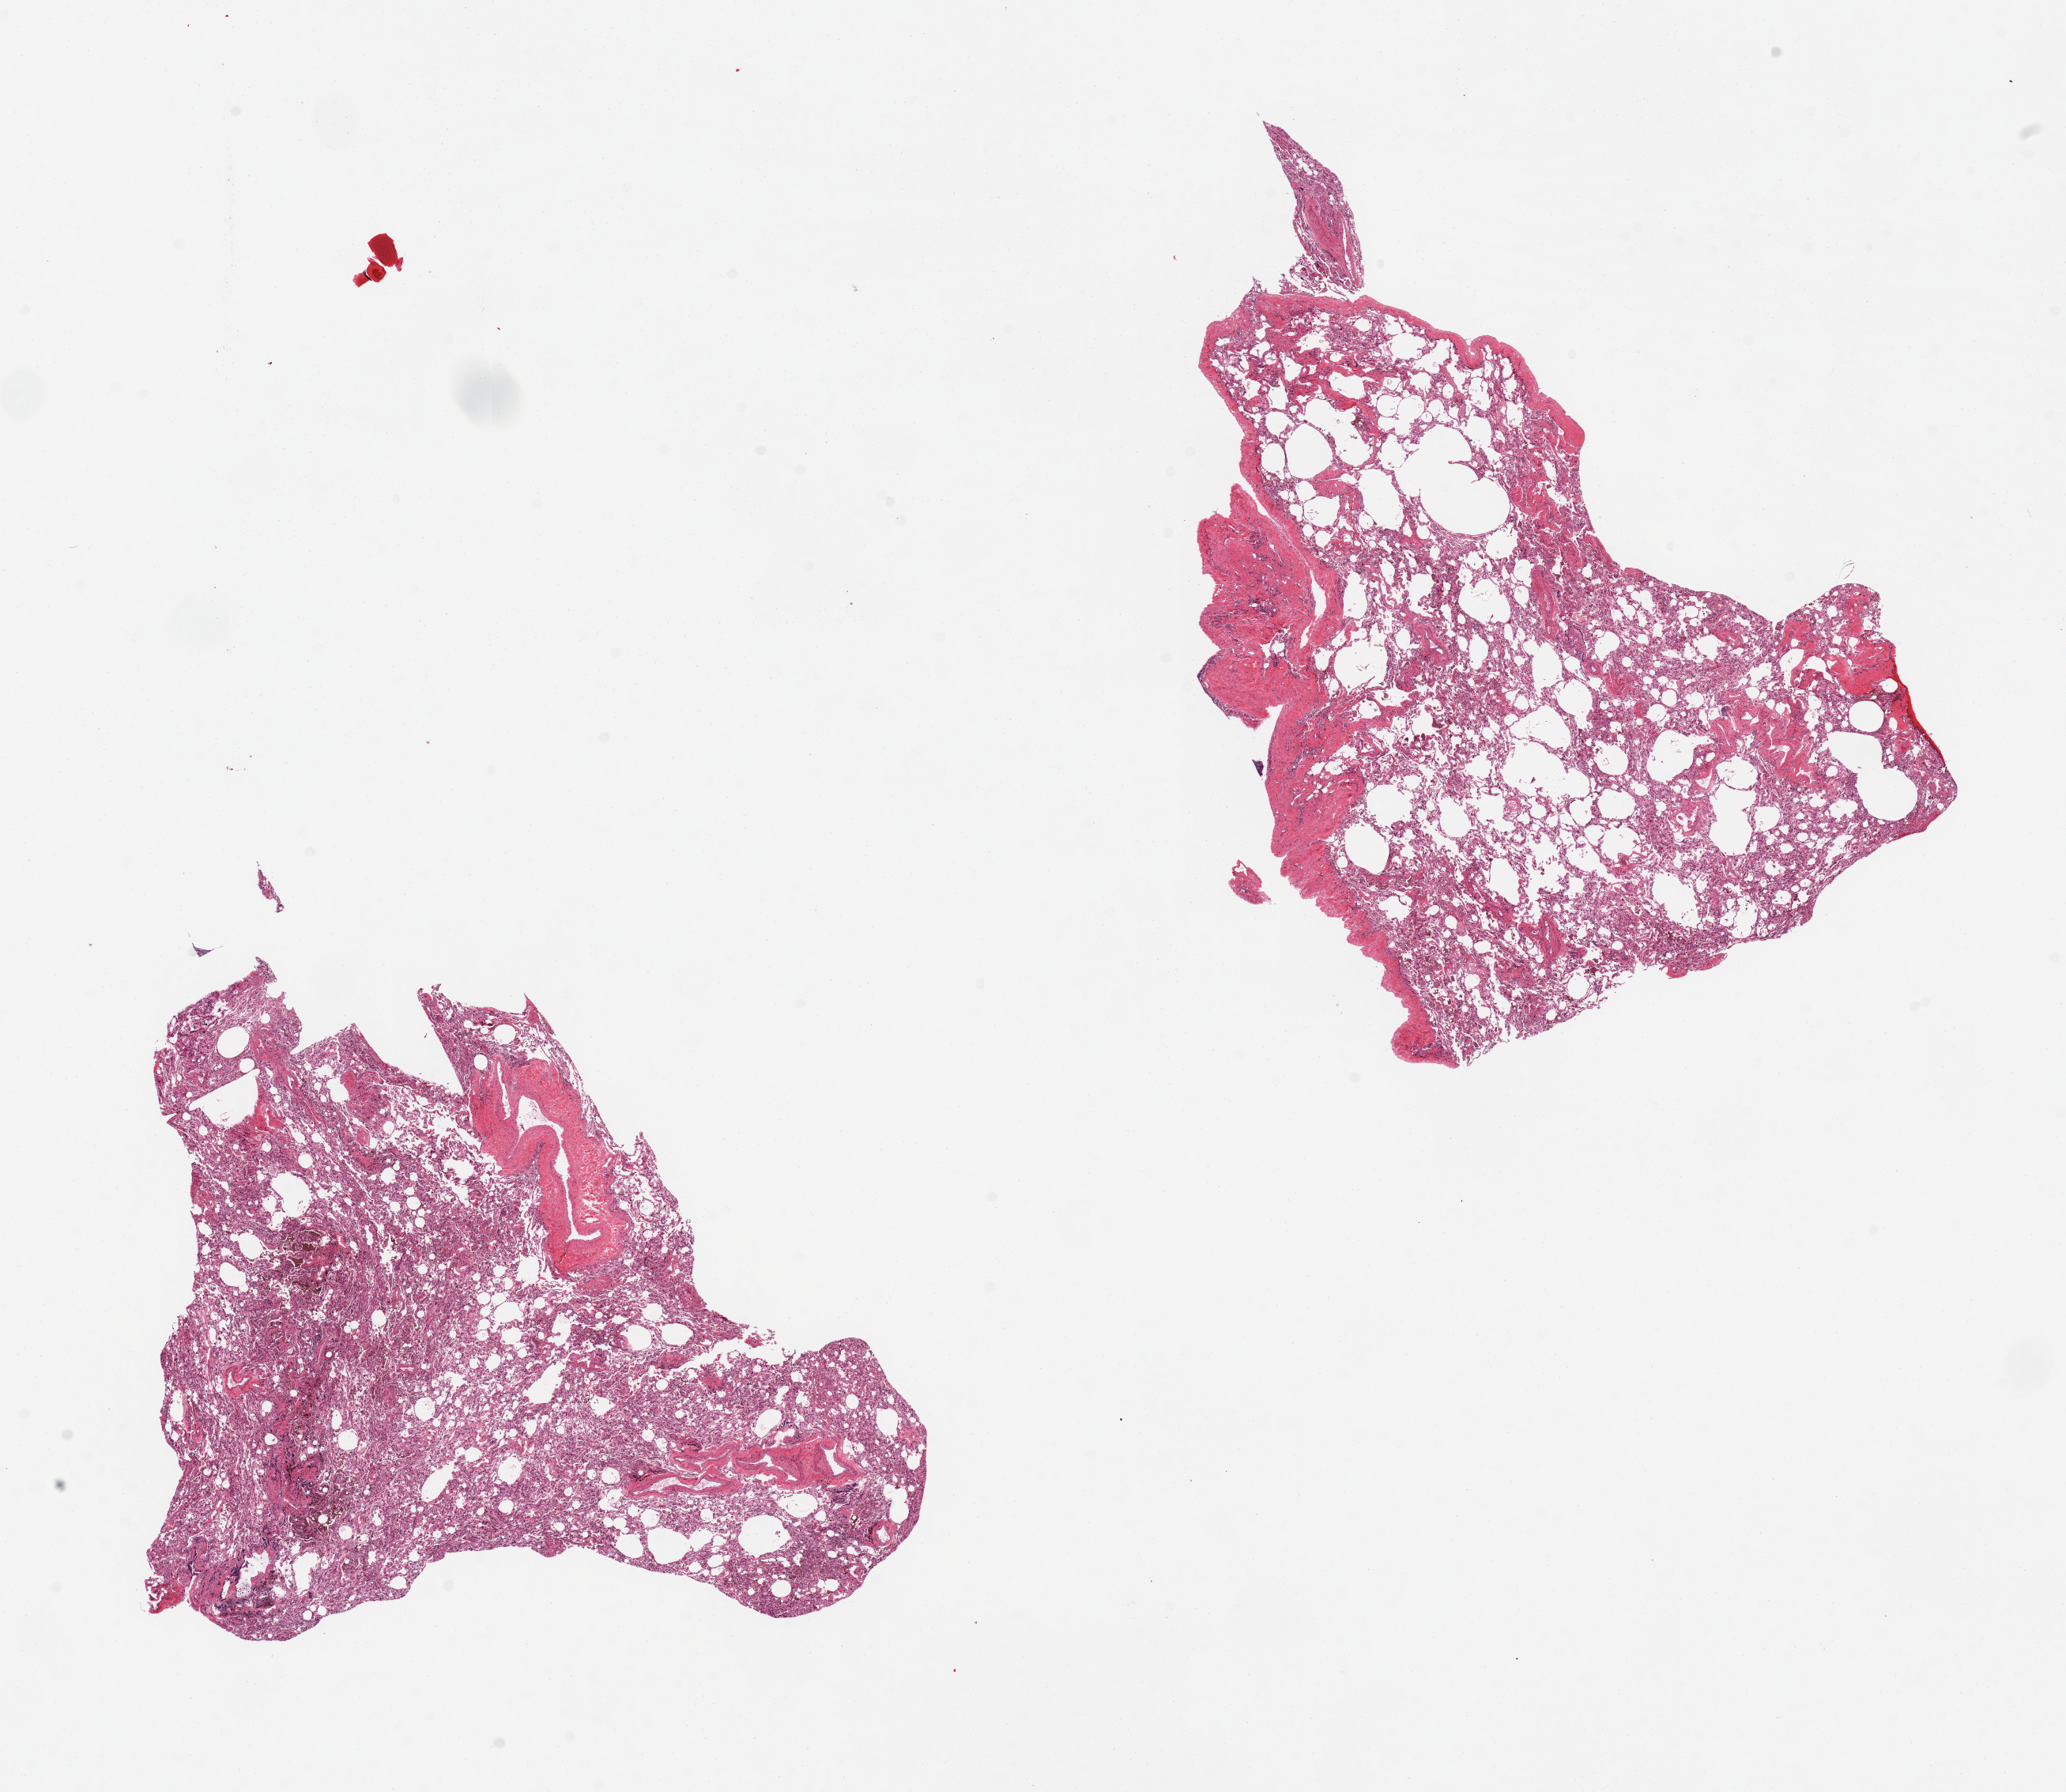
Haematoxylin and eosin whole-slide image, brightfield, low-resolution overview of the scanned area, about 20.7 x 17.9 mm (acquisition: 20x scan). PAXgene-fixed paraffin-embedded (PFPE) section. Section of lung (target tissue). Donor tissue sample.
Reviewer comment on this tissue sample: 2 pieces; emphysema & atelectasis.